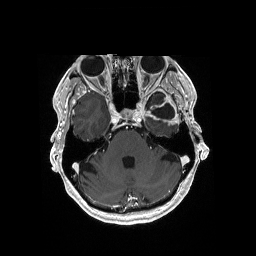
Brain MRI from a brain-tumour surgery series, one axial slice. Slice 128 of 176 in the series (ordered by position). T1-weighted post-contrast. 256 × 256 image matrix, field of view 256 × 256 mm. From the clinical record (not read from this slice): histopathology: Glioblastoma; WHO grade: 4; IDH mutation: no; tumour location: Left Medial Temporal.
Annotated regions visible in this slice (outlined manually by an expert reader):
- previous resection cavity: bounding box <152,103,175,119> (left, top, right, bottom; pixels)
- tumour: <151,114,180,126>